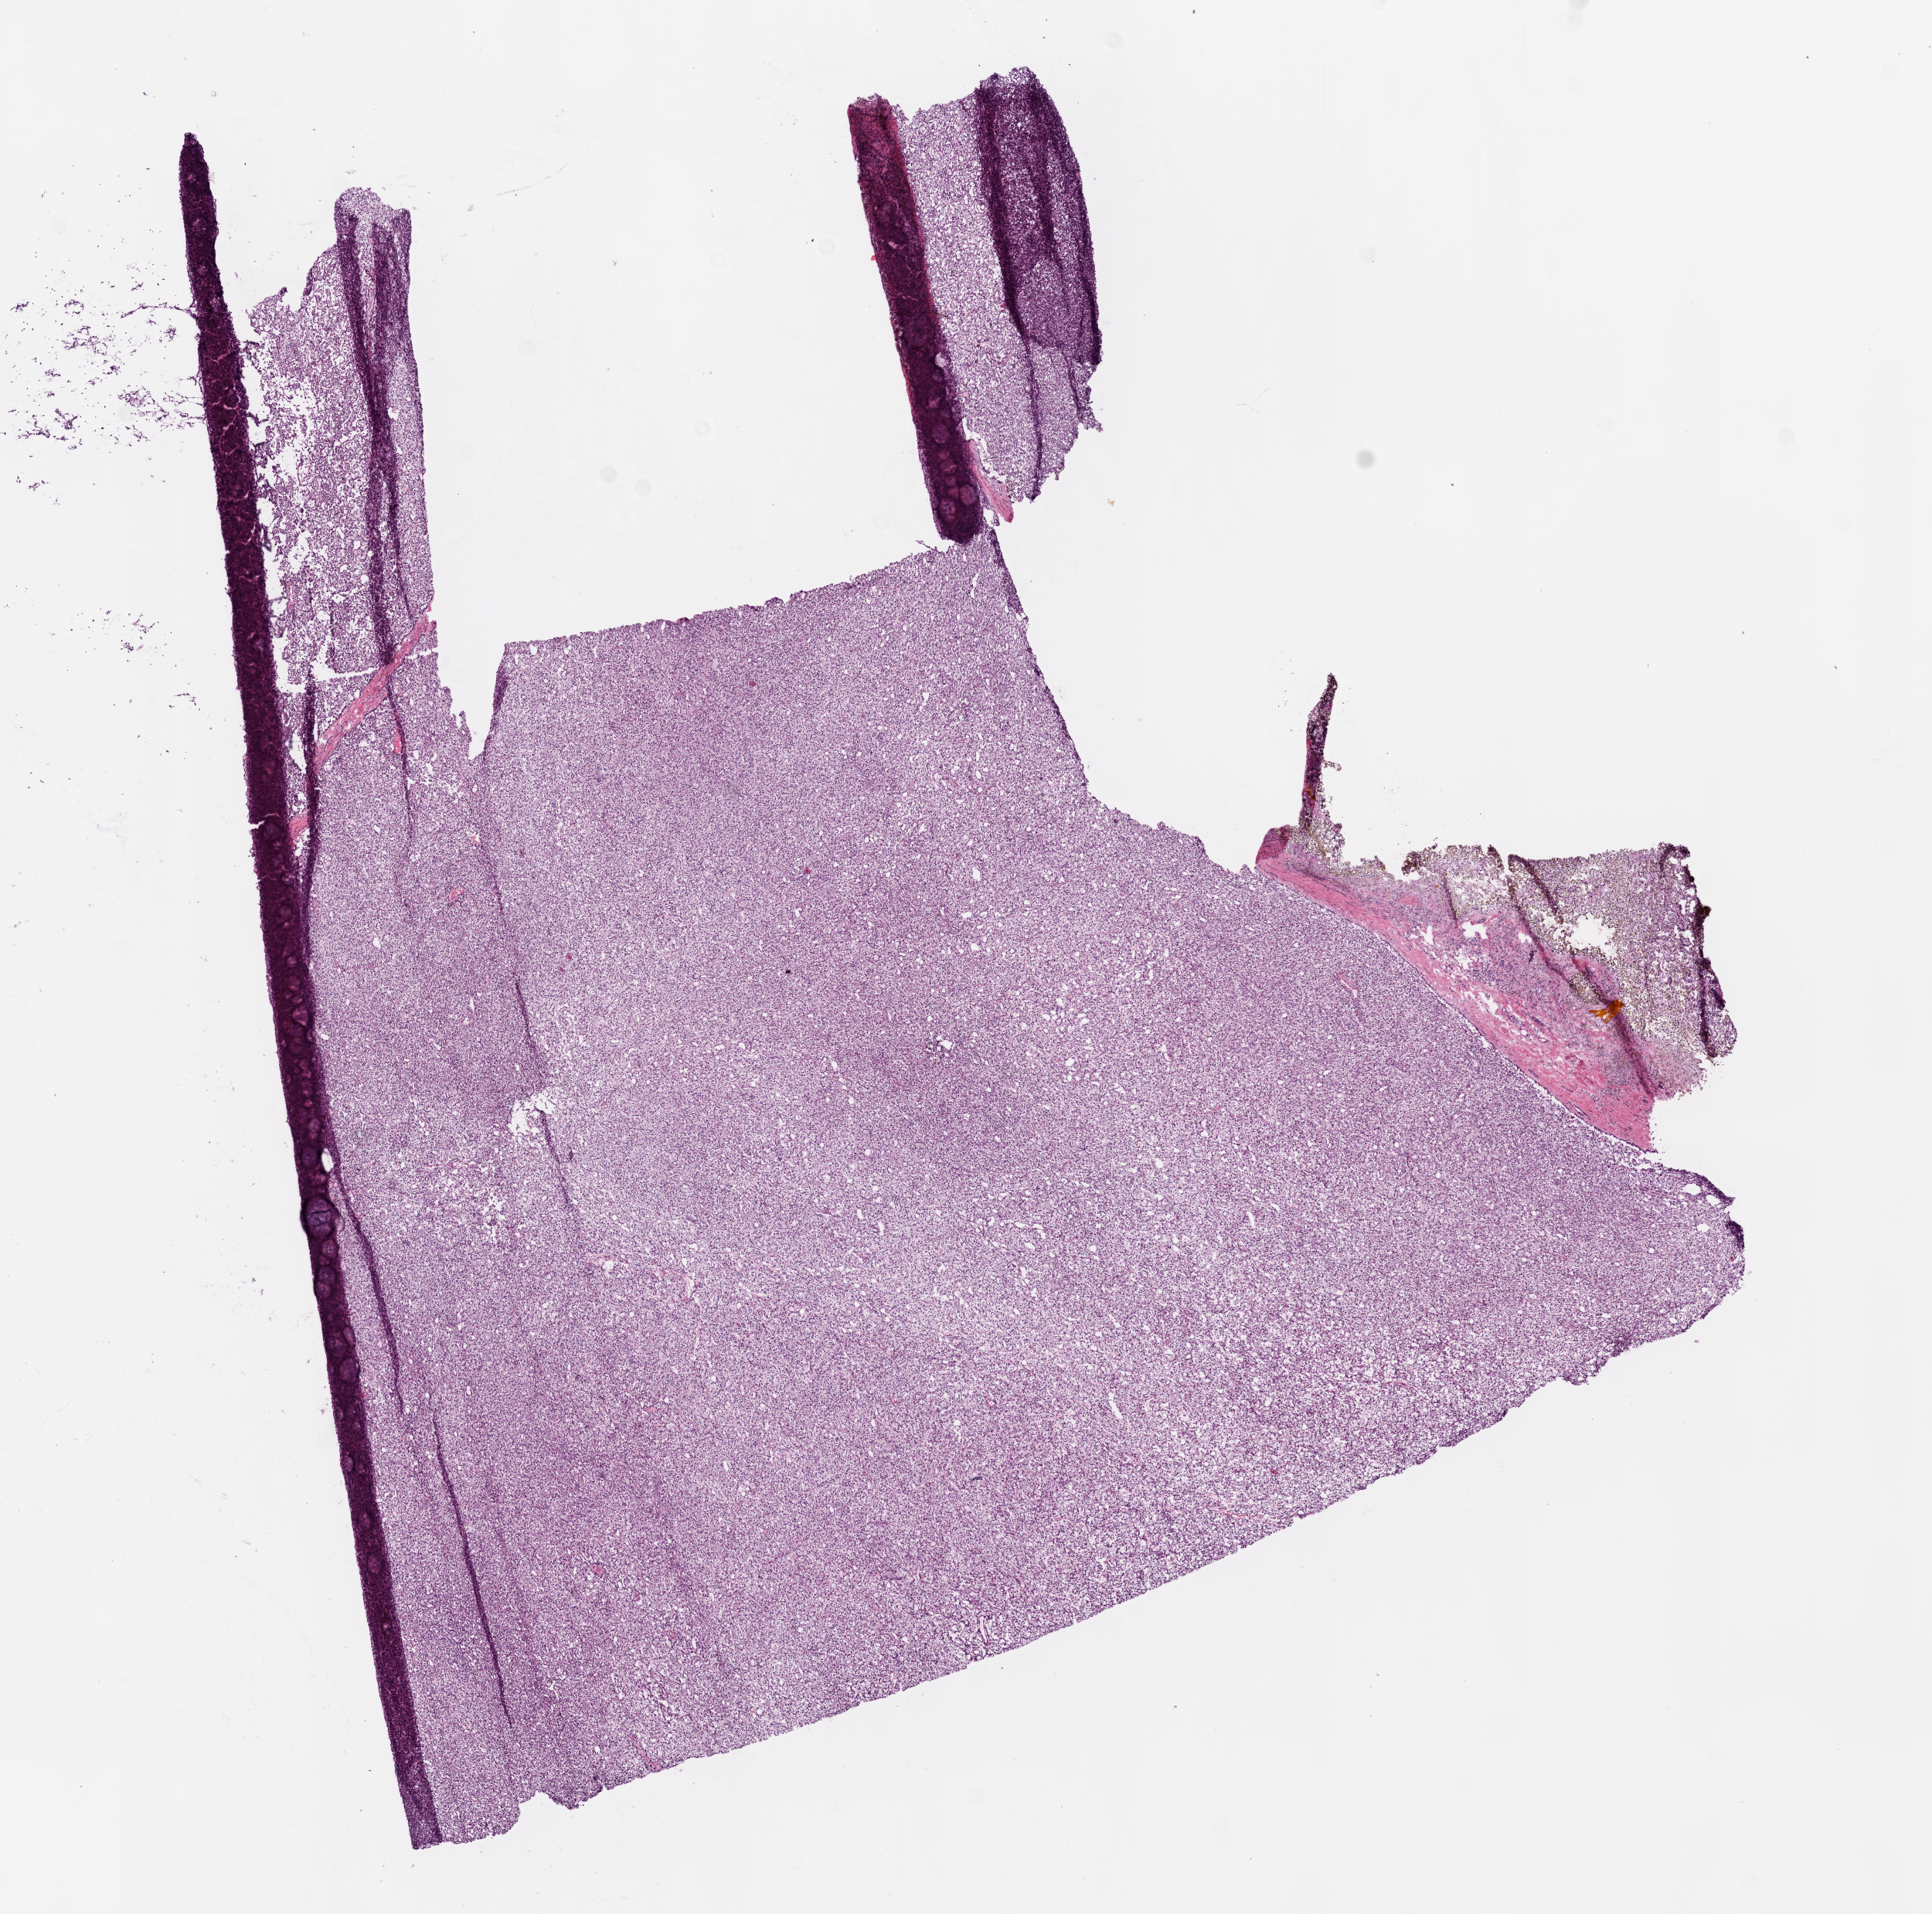
H&E whole-slide image, shown as a low-resolution overview of the whole scanned area (about 10.0 x 9.9 mm, acquisition: 20x scan), frozen section from the bottom of the tissue portion, primary tumour sample from the kidney. Patient: male, age at initial diagnosis 50 years. Histologic grade: G2 (moderately differentiated). Composition of this section per pathologist review: tumour cells 87%, tumour nuclei 85%, normal cells 8%, stromal cells 5%, necrosis 0%.
• laterality: left
• TNM: T2 N0 M0
• AJCC pathologic stage: II
• pathologic diagnosis: Clear cell adenocarcinoma, NOS